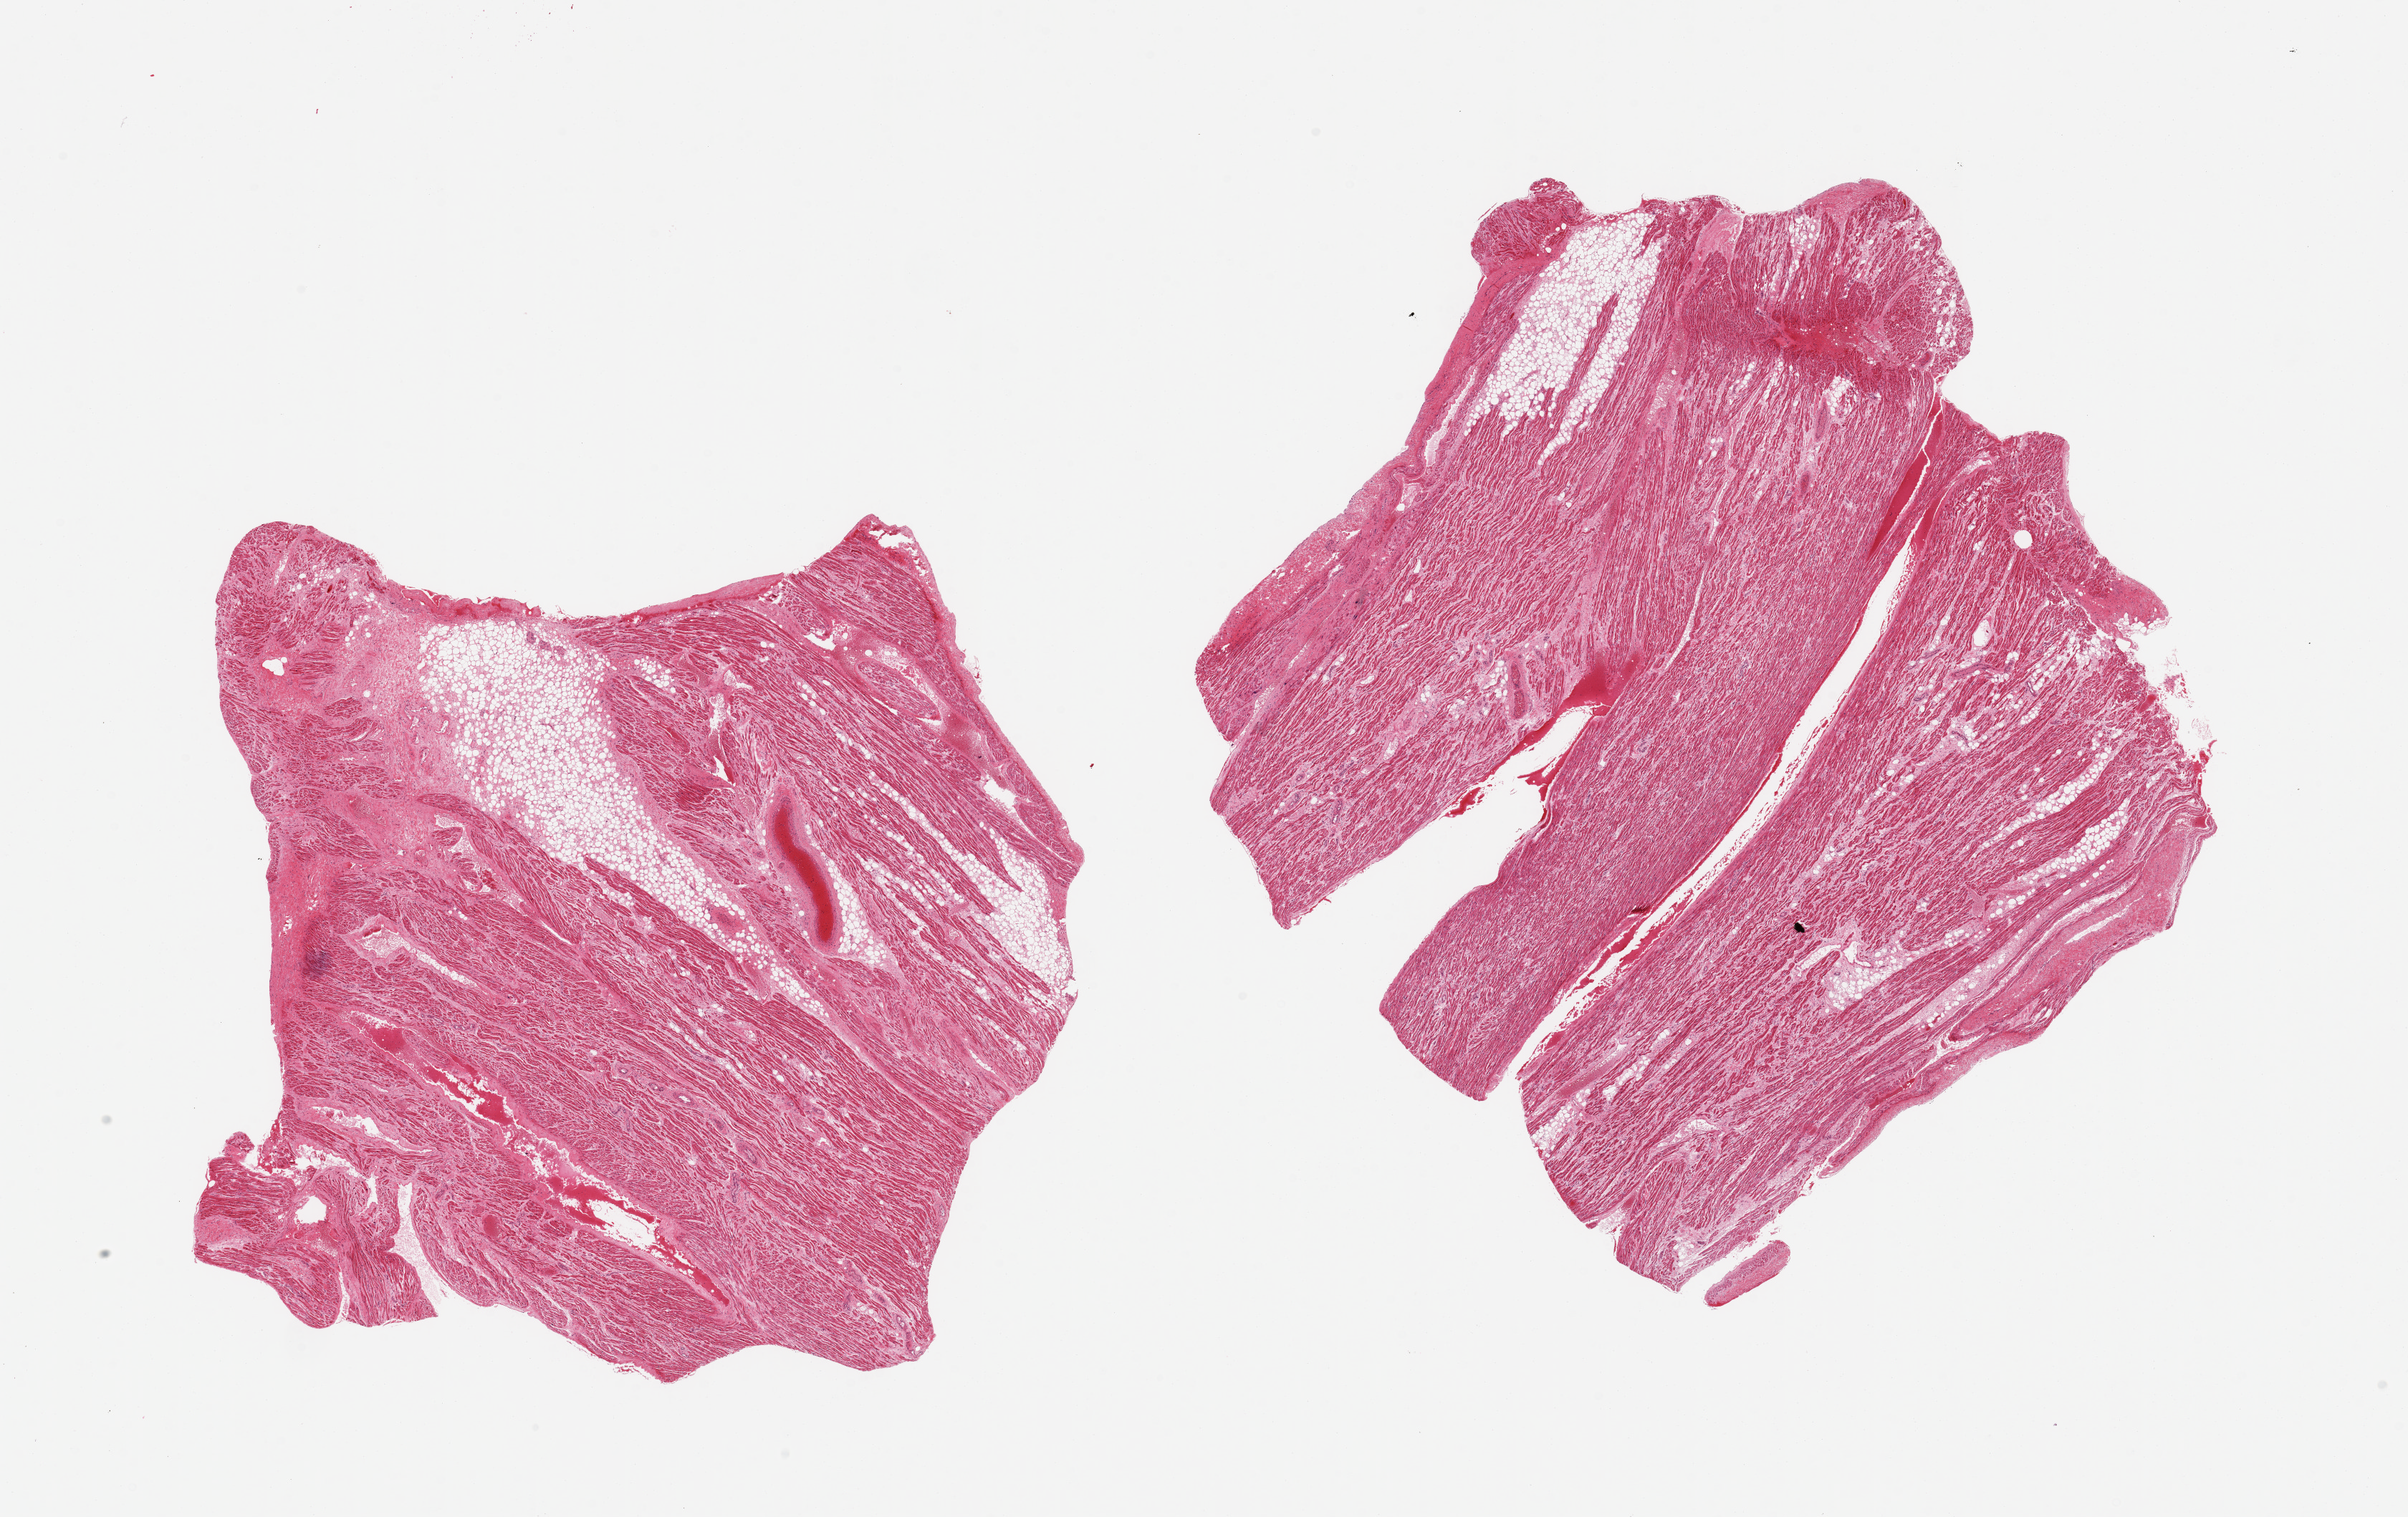
Hematoxylin and eosin (H&E) whole-slide image — shown as a low-resolution overview of the whole scanned area (about 26.6 x 16.7 mm), PAXgene-fixed, paraffin-embedded tissue, target tissue: auricular appendage, tissue donor sample. Donor sex: male.
* review note (as recorded): 2 pieces, no abnormalities